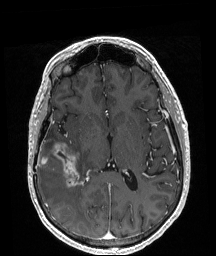
Brain MRI from a brain-tumour surgery series, one axial slice; position 101 of 208 along the scan axis; T1-weighted post-contrast; 1 mm slice thickness; 216 × 256 image matrix, field of view 211 × 250 mm. From the clinical record (not read from this slice): histopathology: Astrocytoma; WHO grade: 4; IDH mutation: yes; tumour location: Right Temporal.
Outlined on this slice (outlined manually by an expert reader):
- tumour: bounding box [x1, y1, x2, y2] px = [38, 143, 79, 188]